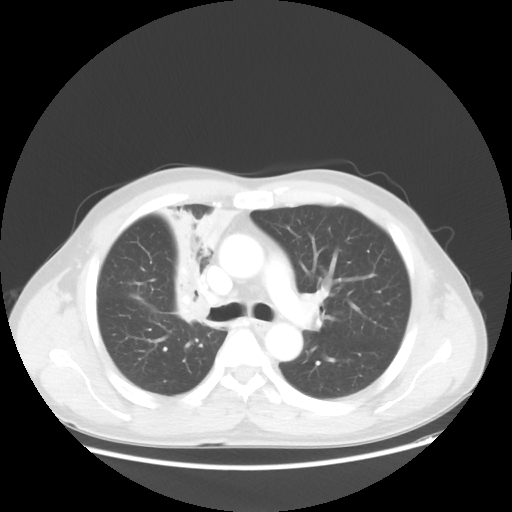
Chest CT, one axial slice. Slice 35 of 56 in the series (ordered by position). Lung window (W 1500 / L -600 HU). 5 mm slice thickness. 512 × 512 image matrix. Male patient, age 60 years. Case-level facts recorded for this patient, not image findings: clinical TNM (as recorded): T2a N1 M0.
Structures marked on this image (bounding box drawn by a radiologist):
- lung tumour (recorded histology: squamous cell carcinoma): bounding box (x1, y1, x2, y2) in pixels: (151, 192, 258, 330)